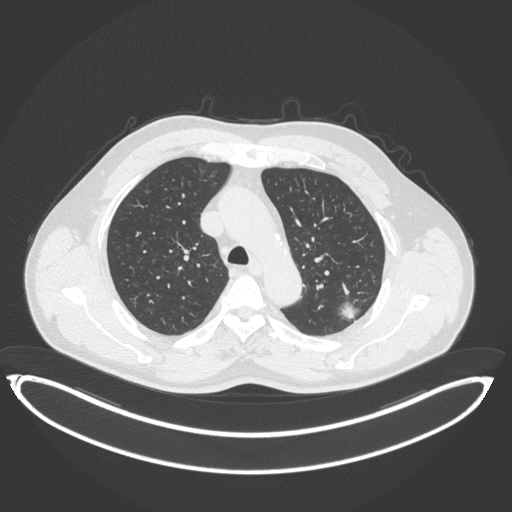
Chest CT, one axial slice; position 264 of 399 along the scan axis; reconstruction kernel B31f; lung window (W 1500 / L -600 HU); 512 × 512 image matrix, field of view 469 × 469 mm. Patient: male, 58 years. Case-level facts recorded for this patient, not image findings: clinical TNM (as recorded): T1c N0 M0; histopathological grade: G1-2.
Structures marked on this image (rectangle marked by the reading radiologist):
- lung tumour (recorded histology: adenocarcinoma): box from (x=337, y=295) to (x=365, y=325) px